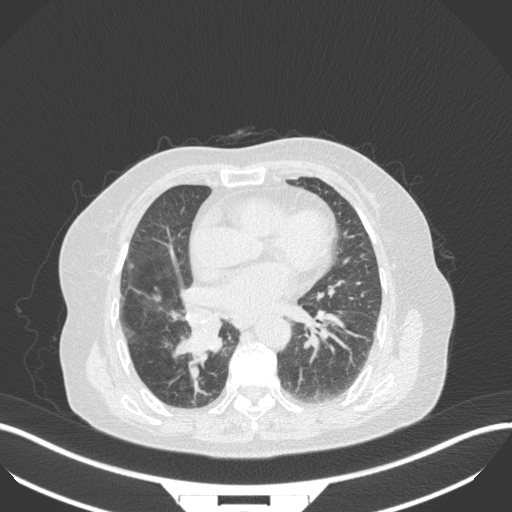
Chest CT, one axial slice; slice 143 of 329 in the series (ordered by position); reconstruction kernel B31f; 120 kVp; lung window (W 1500 / L -600 HU); 1 mm slice thickness; 512 × 512 image matrix, field of view 400 × 400 mm. Patient: female, 75 years. From the clinical record (not read from this slice): clinical TNM (as recorded): T1b N0 M1a; histopathological grade: G1.
Structures marked on this image (bounding box drawn by a radiologist):
- lung tumour (recorded histology: squamous cell carcinoma): bounding box <170,309,223,360> (left, top, right, bottom; pixels)